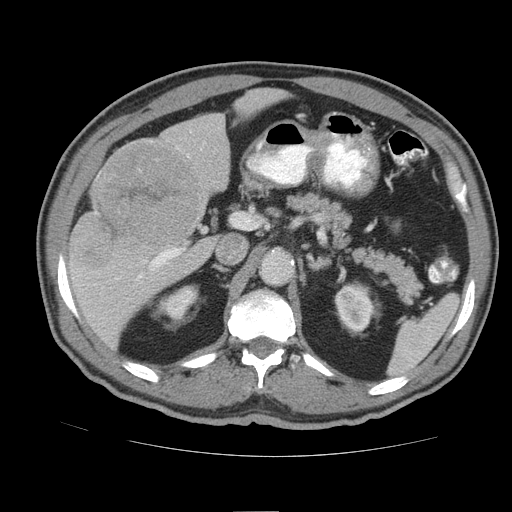
Contrast-enhanced abdominal CT (liver protocol), one axial slice. Slice 50 of 105 in the series (ordered by position). 140 kVp. Soft-tissue window (W 400 / L 40 HU). 512 × 512 image matrix. Case-level facts recorded for this patient, not image findings: diagnosis: hepatocellular carcinoma (patient treated with transarterial chemoembolisation; whether this scan precedes or follows treatment is not stated here); TNM stage (as recorded): Stage-IIIB; Child-Pugh class: A; tumour nodularity: multinodular.
Annotated regions visible in this slice (semi-automatic segmentation, software-assisted and operator-edited):
- liver parenchyma outside the tumour (the mass and vessels are separate outlines, so this box may not span the whole liver): bounding box <68,88,282,348> (left, top, right, bottom; pixels)
- mass: <73,142,201,268>
- liver vessels: <116,248,184,280>